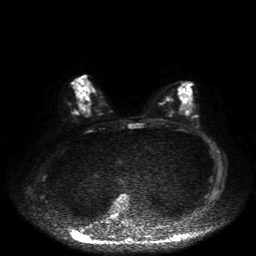
Breast MRI, one axial slice. Position 25 of 50 along the scan axis. Diffusion-weighted series; image 2 of 4 stored at this slice position (different b-values; order by instance number). 1.5 T. 4 mm slice thickness. 256 × 256 image matrix, field of view 360 × 360 mm. Female patient.
Outlined on this slice (outlined manually by an expert reader):
- tumour on diffusion-weighted imaging: bounding box (x1, y1, x2, y2) in pixels: (79, 107, 85, 114)